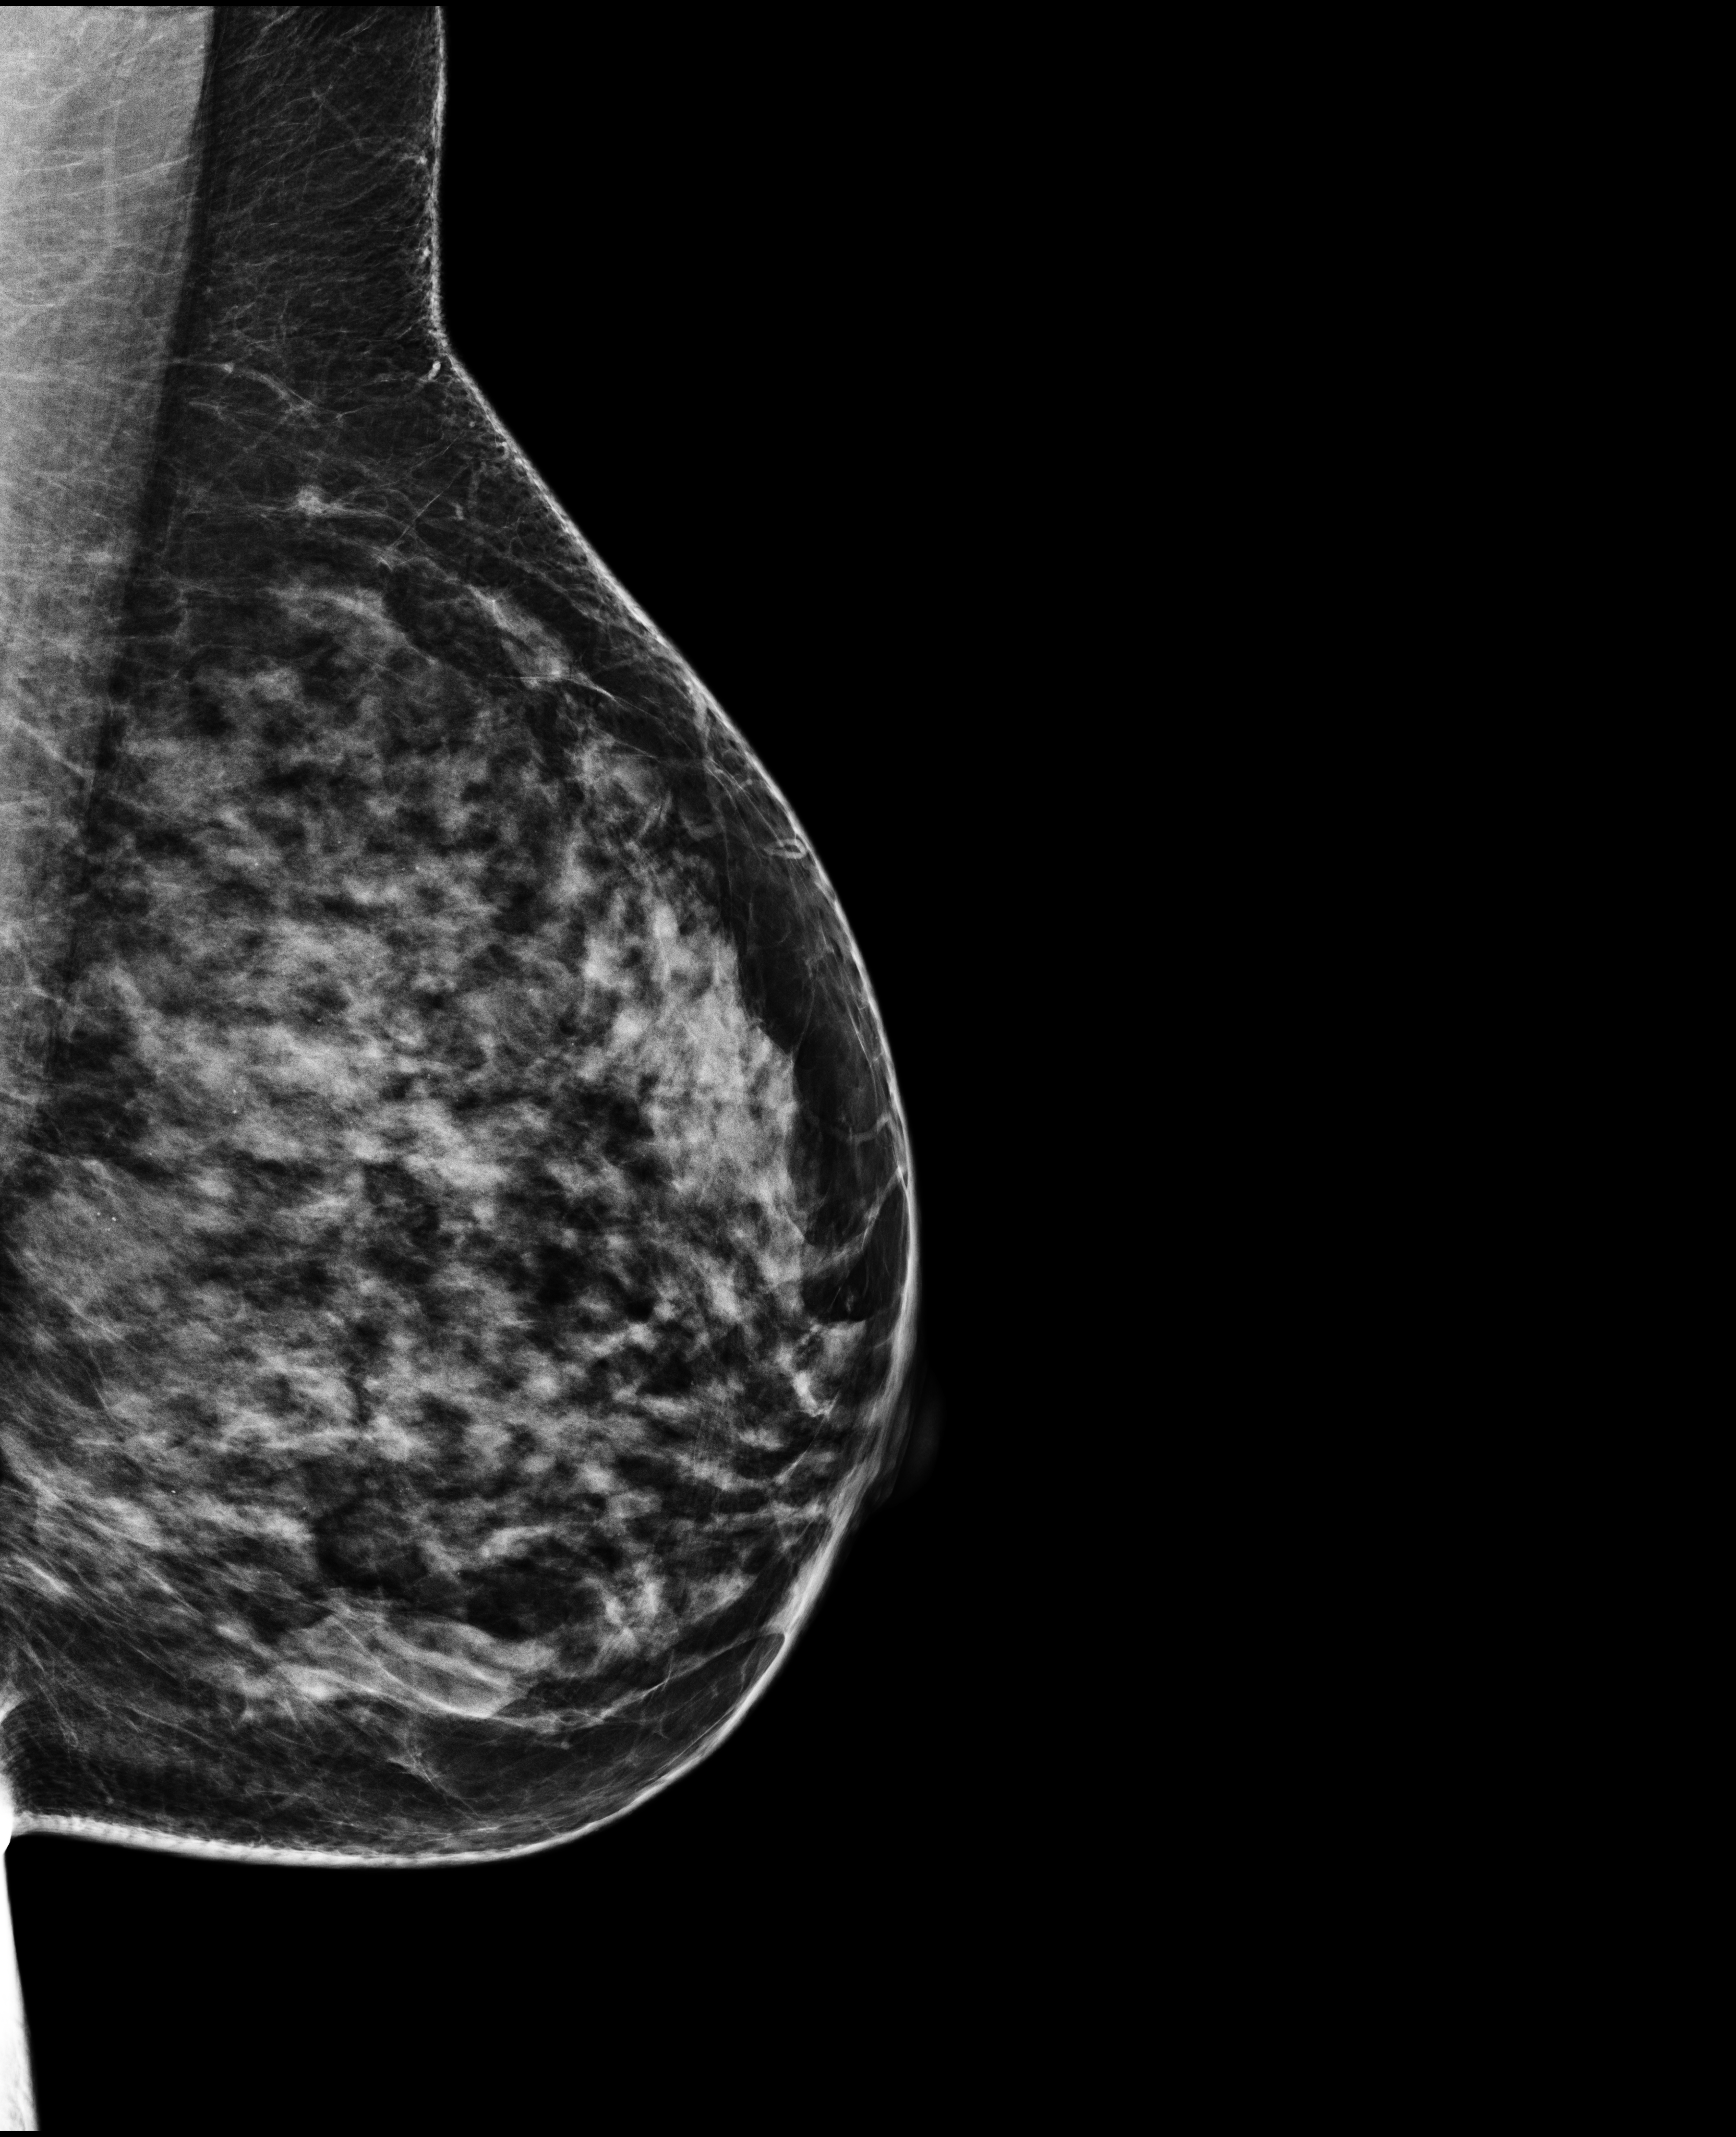
Full-field digital mammogram (FFDM), left breast, MLO view, screening examination, compressed breast thickness 68 mm. Female patient, age 51 years.
- BI-RADS breast density category at the screening exam (both breasts, scale 1–4): 3
- final BI-RADS category for the screening round (tomosynthesis exam, both breasts): category 1
- recall: no recall after this screen